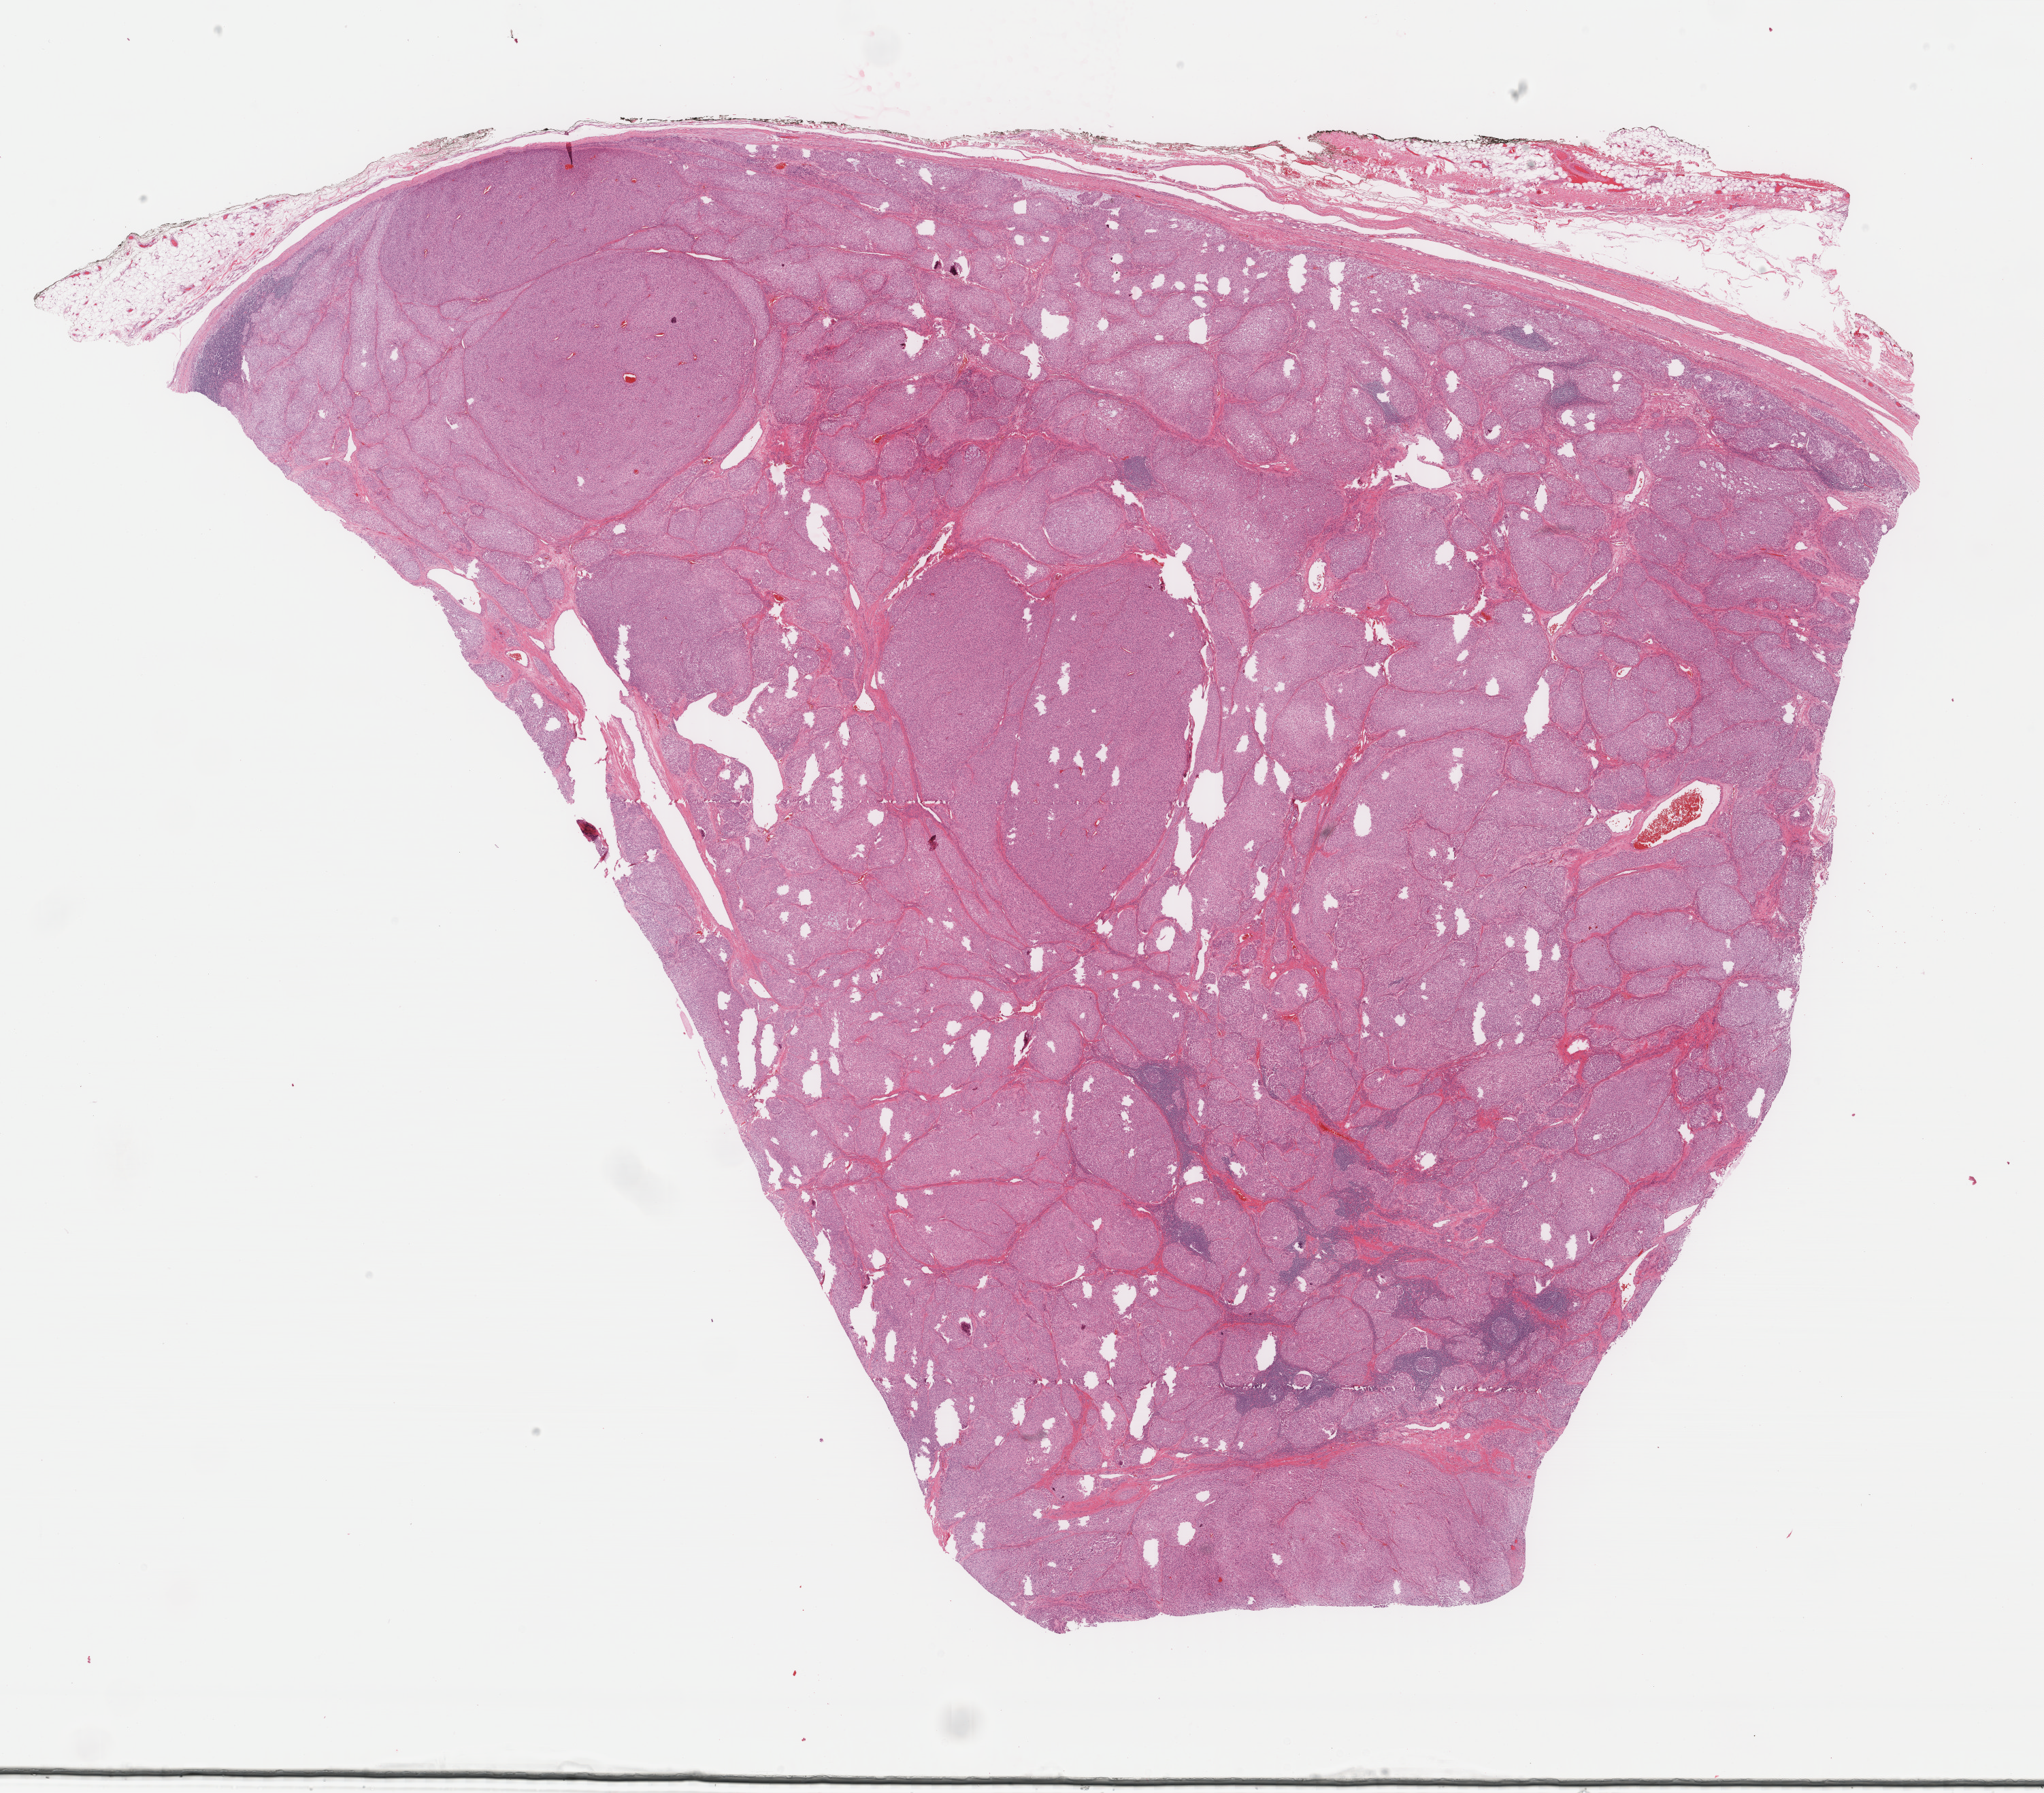
H&E-stained whole-slide image — whole scanned area (about 23.8 x 20.9 mm, acquisition: 40x scan) shown as a low-resolution overview, formalin-fixed paraffin-embedded (FFPE) diagnostic section, primary tumour sample from the skin. Patient: male, age at initial diagnosis 35 years.
Histologic diagnosis: Malignant melanoma, NOS.